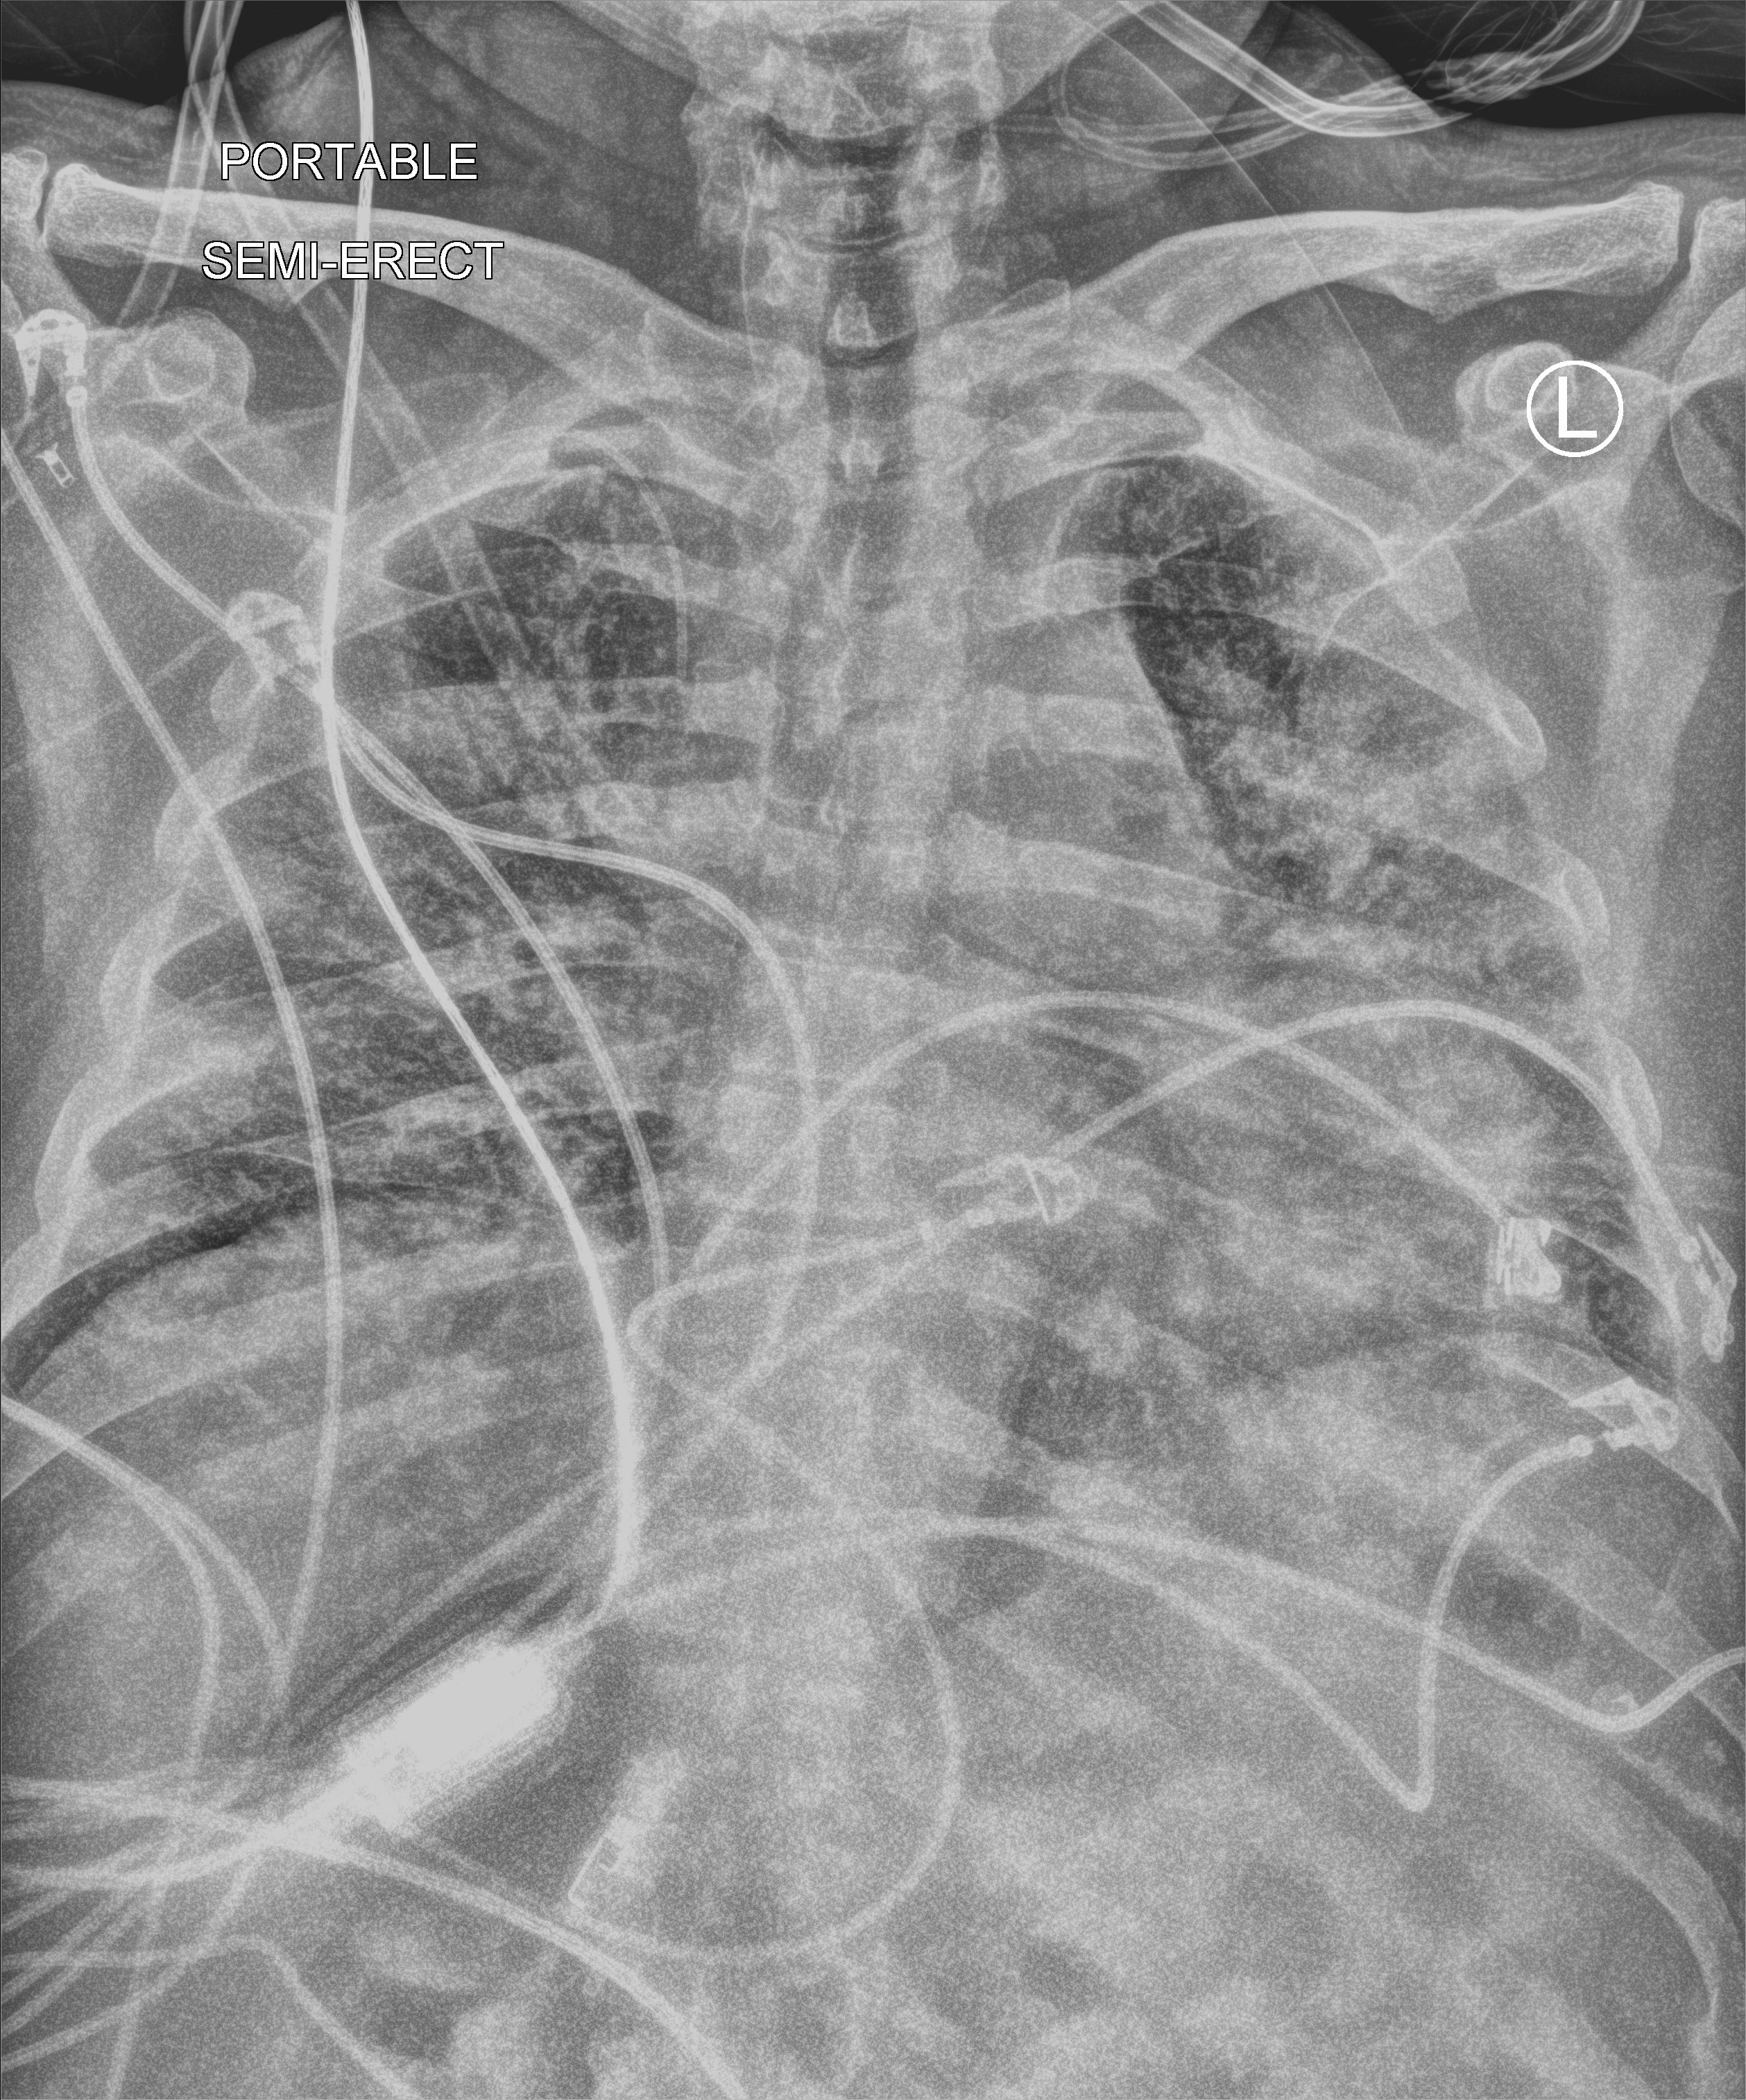
Chest X-ray (portable). Patient hospitalised with COVID-19; male, aged 18–59 years.
Hospital-stay facts (about this admission, not read from this image; timing relative to this image not recorded): mechanically ventilated during this hospital stay: yes; smoking status (admission record): former.